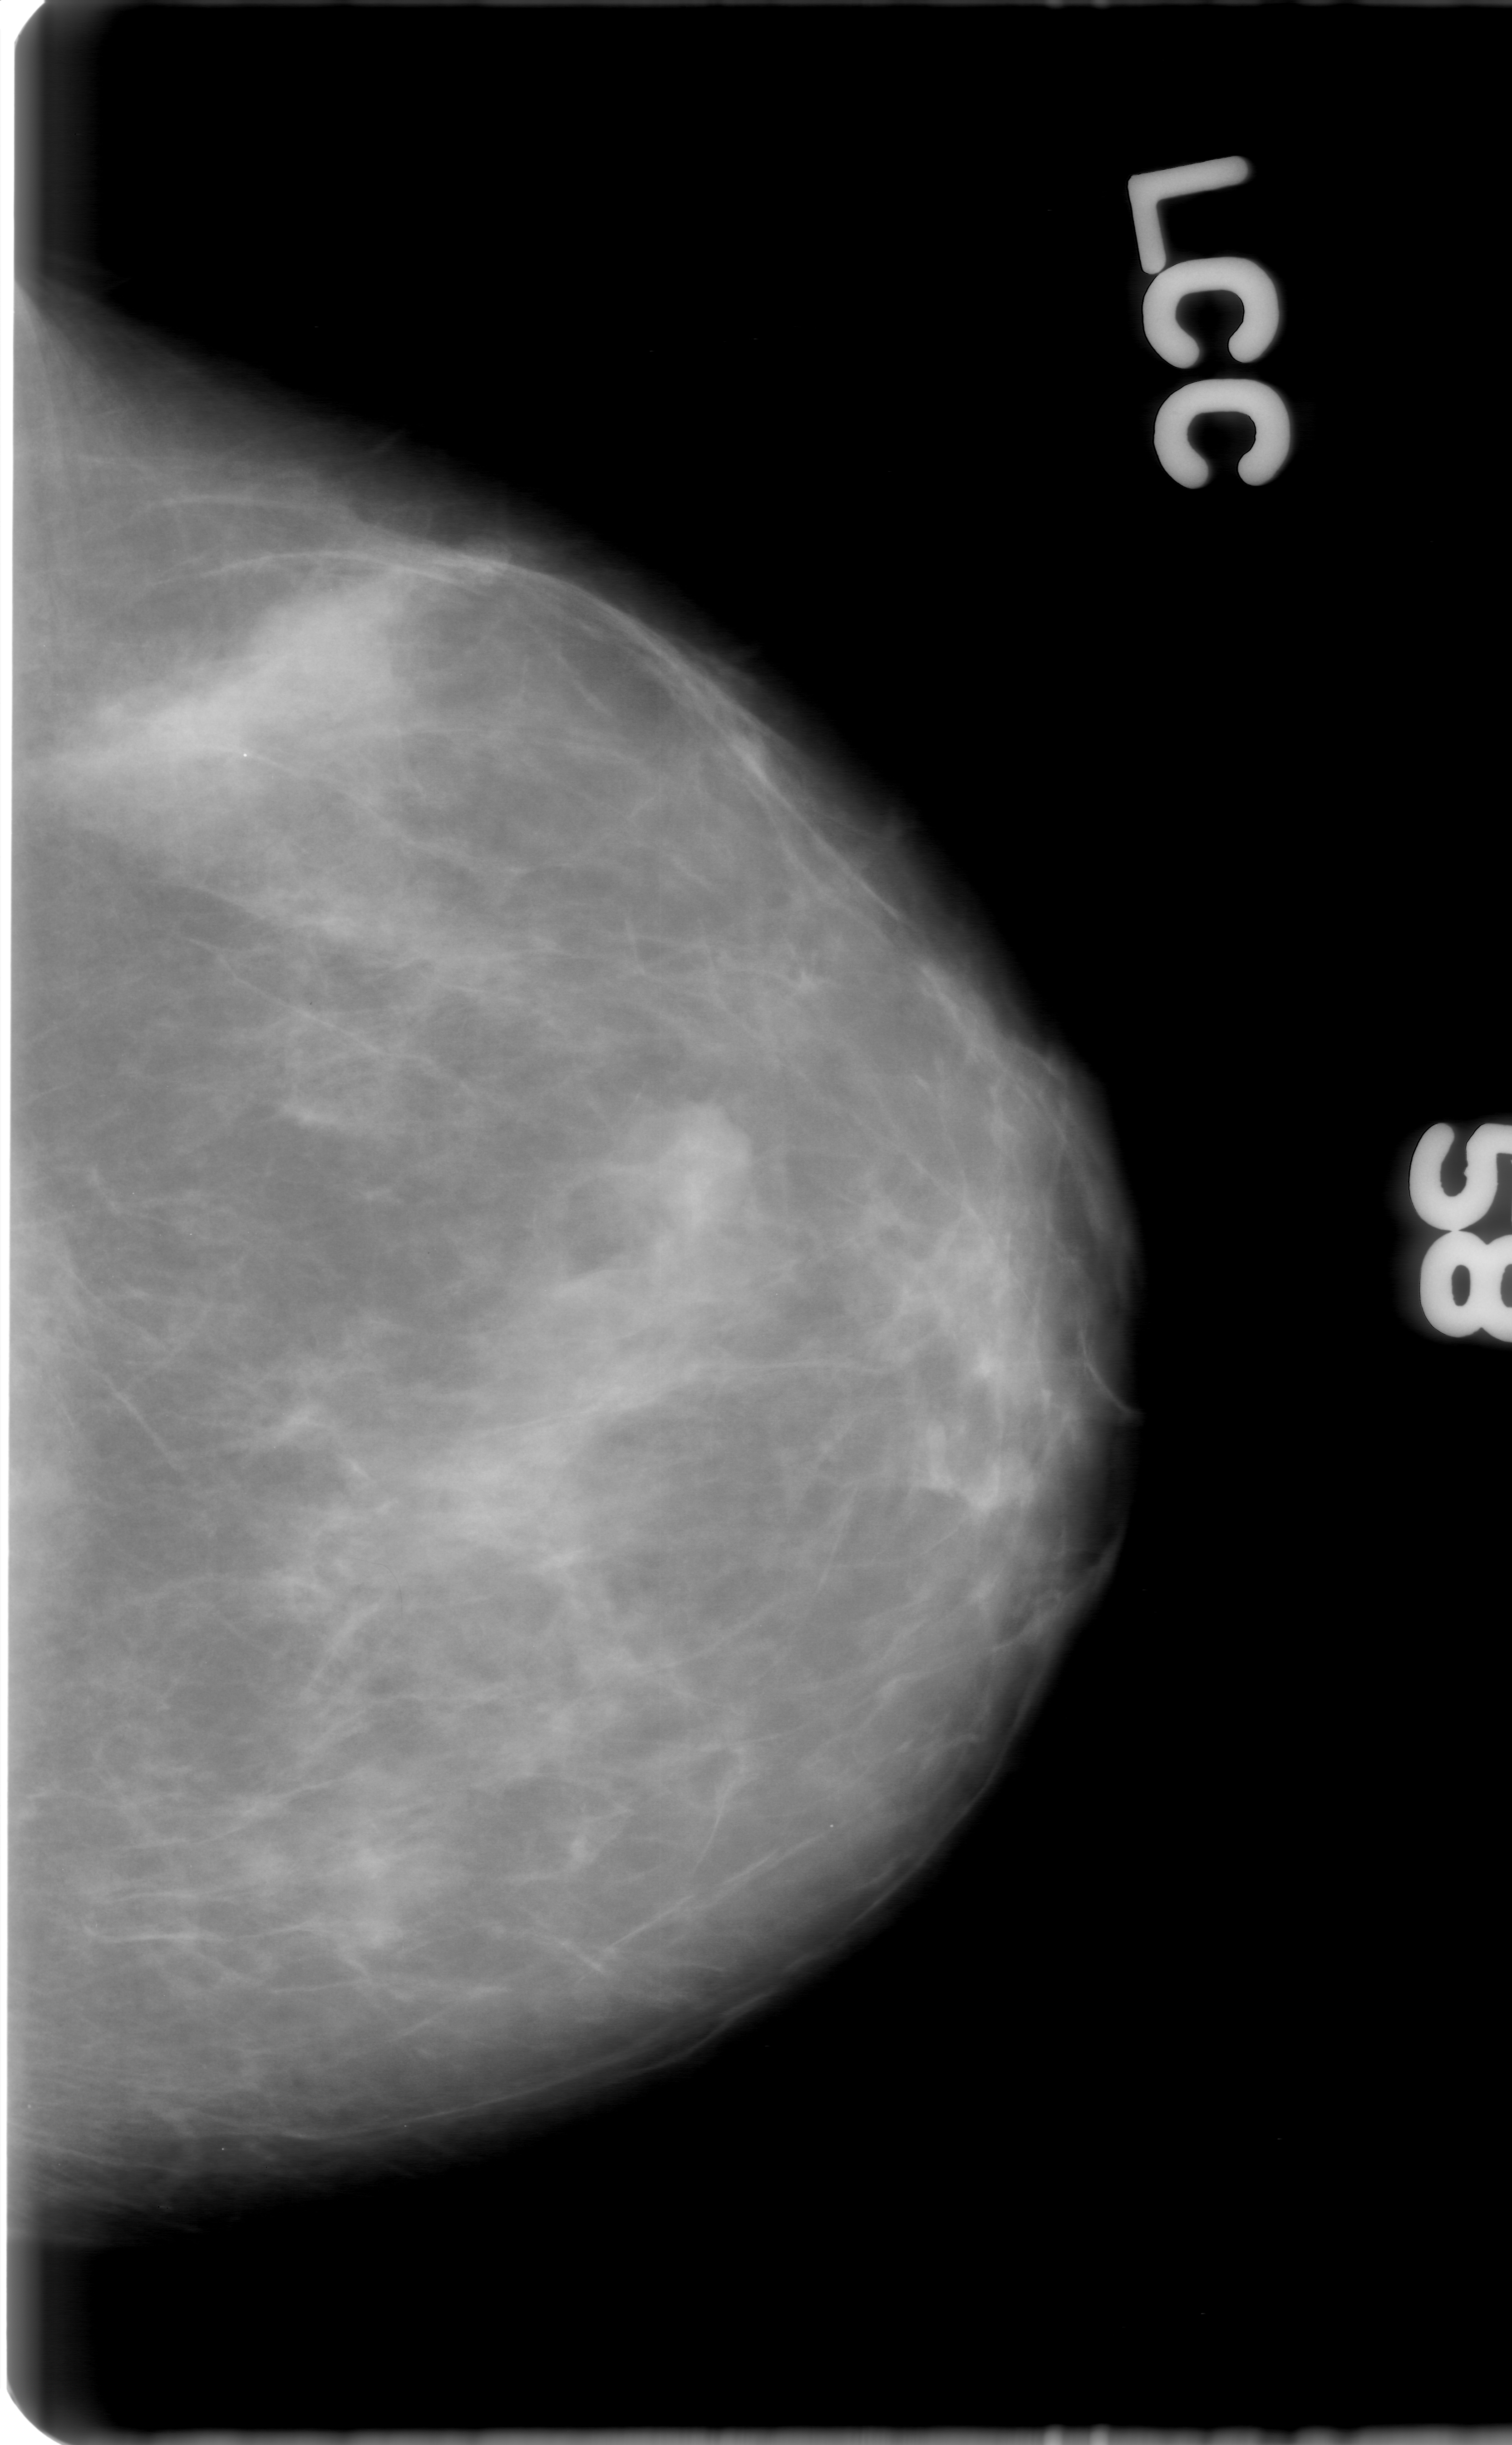
Digitized screen-film mammogram. Left breast. Craniocaudal (CC) view. 1512 × 2445 image matrix.
Expert-marked regions of interest on this film, with their recorded descriptors:
- mass, shape oval, margins obscured; BI-RADS assessment category 0 (incomplete: needs additional imaging); subtlety rating 5 on a 1 (subtle) to 5 (obvious) scale; pathology (as recorded): benign: box from (x=591, y=1090) to (x=759, y=1242) px